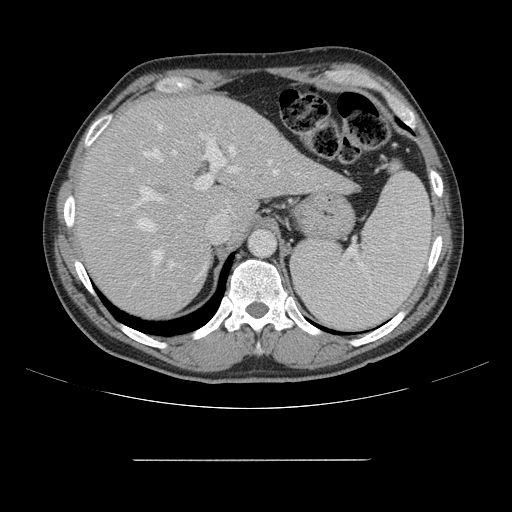
Contrast-enhanced abdominal CT, one axial slice; slice 111 of 164 in the series (ordered by position); 120 kVp; intravenous contrast given; soft-tissue window (W 400 / L 40 HU); 2.5 mm slice thickness; 512 × 512 image matrix, field of view 404 × 404 mm. Male patient, age 54 years. From the clinical record (not read from this slice): diagnosis: colorectal cancer liver metastases, imaged before liver resection; multiple liver metastases: yes; largest metastasis: 1 cm; disease in both lobes: no.
Annotated regions visible in this slice (manually delineated by an expert):
- hepatic veins: bounding box (x1, y1, x2, y2) in pixels: (139, 125, 279, 276)
- liver: (77, 97, 350, 318)
- planned liver remnant (the part of the liver to remain after resection): (77, 96, 244, 318)
- portal vein (with intrahepatic branches): (119, 135, 237, 288)